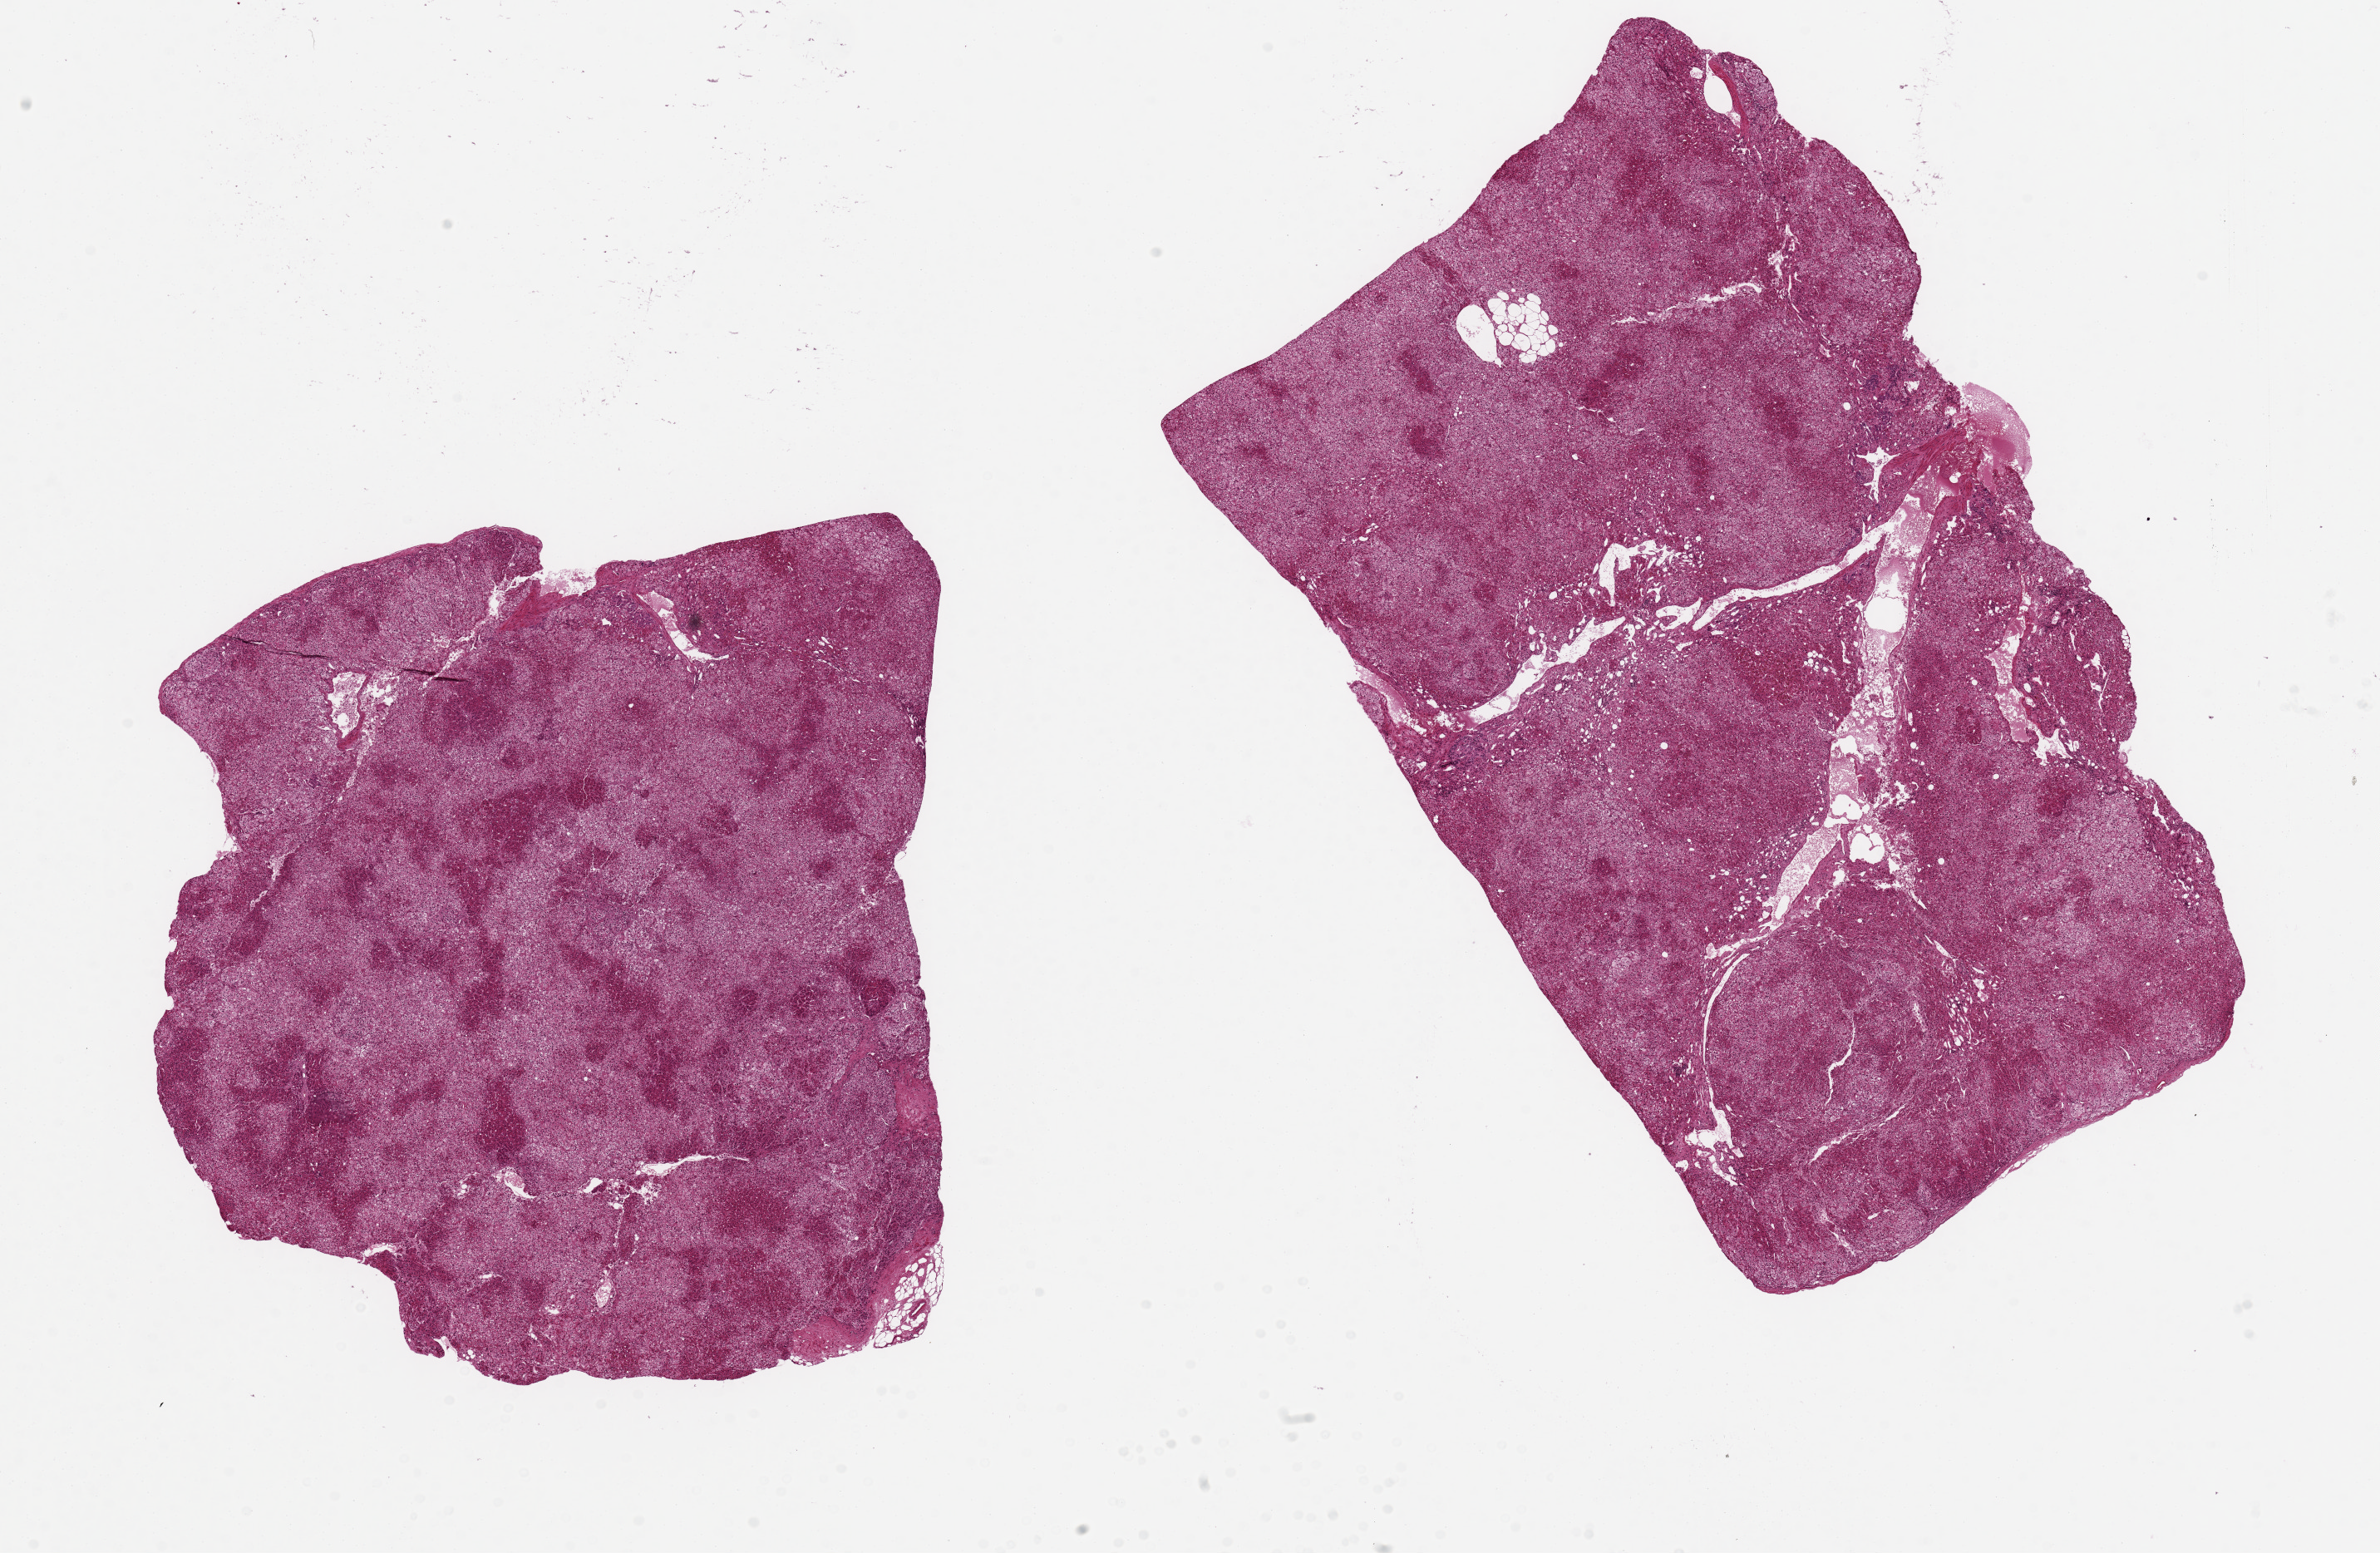
Haematoxylin and eosin whole-slide image, whole scanned area (about 22.6 x 14.8 mm) shown as a low-resolution overview. PAXgene-fixed, paraffin-embedded tissue. Sampled site (target tissue): adrenal gland. Donor tissue sample. Donor sex: male.
Review note (as recorded): 2 pieces 10x6 & 8x7 mm; cortex.